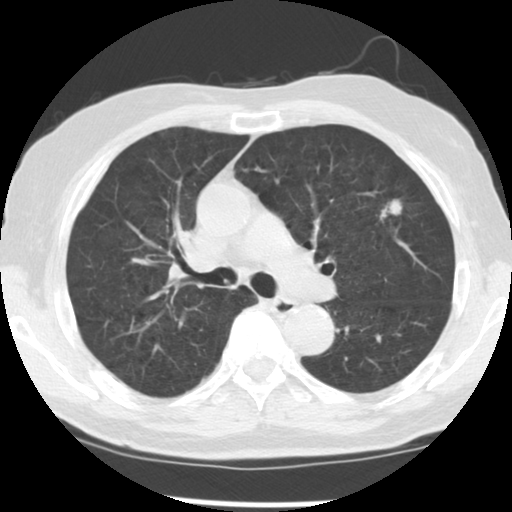
Low-dose screening chest CT, one axial slice; slice 81 of 131 in the series (ordered by position); reconstruction kernel STANDARD; 140 kVp; lung window (W 1500 / L -600 HU); 2.5 mm slice thickness; 512 × 512 image matrix, field of view 330 × 330 mm.
Outlined on this slice (expert manual segmentation):
- lesion 1 (tumor, upper lobe of left lung): box from (x=380, y=200) to (x=402, y=219) px